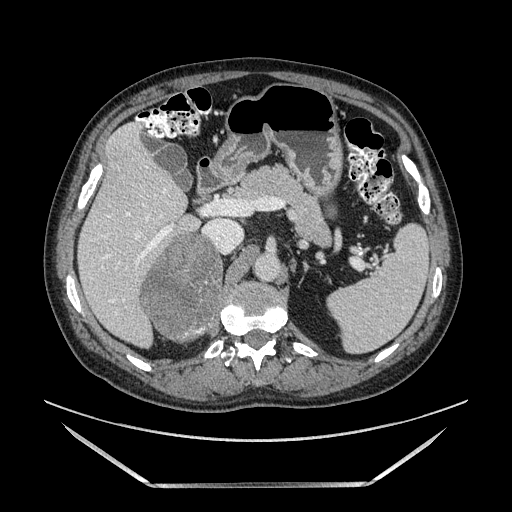
Contrast-enhanced abdominal CT, one axial slice. Position 87 of 185 along the scan axis. Soft-tissue window (W 400 / L 40 HU). 1.25 mm slice thickness. 512 × 512 image matrix, field of view 440 × 440 mm. Male patient. Case-level facts recorded for this patient, not image findings: diagnosis: adrenocortical carcinoma; tumour side: right adrenal; tumour size at pathology: 10.3 cm; Ki-67 index: 20 %; stage (as recorded): 3.
Annotated regions visible in this slice (semi-automatically segmented with operator editing):
- mass: box from (x=143, y=232) to (x=222, y=341) px